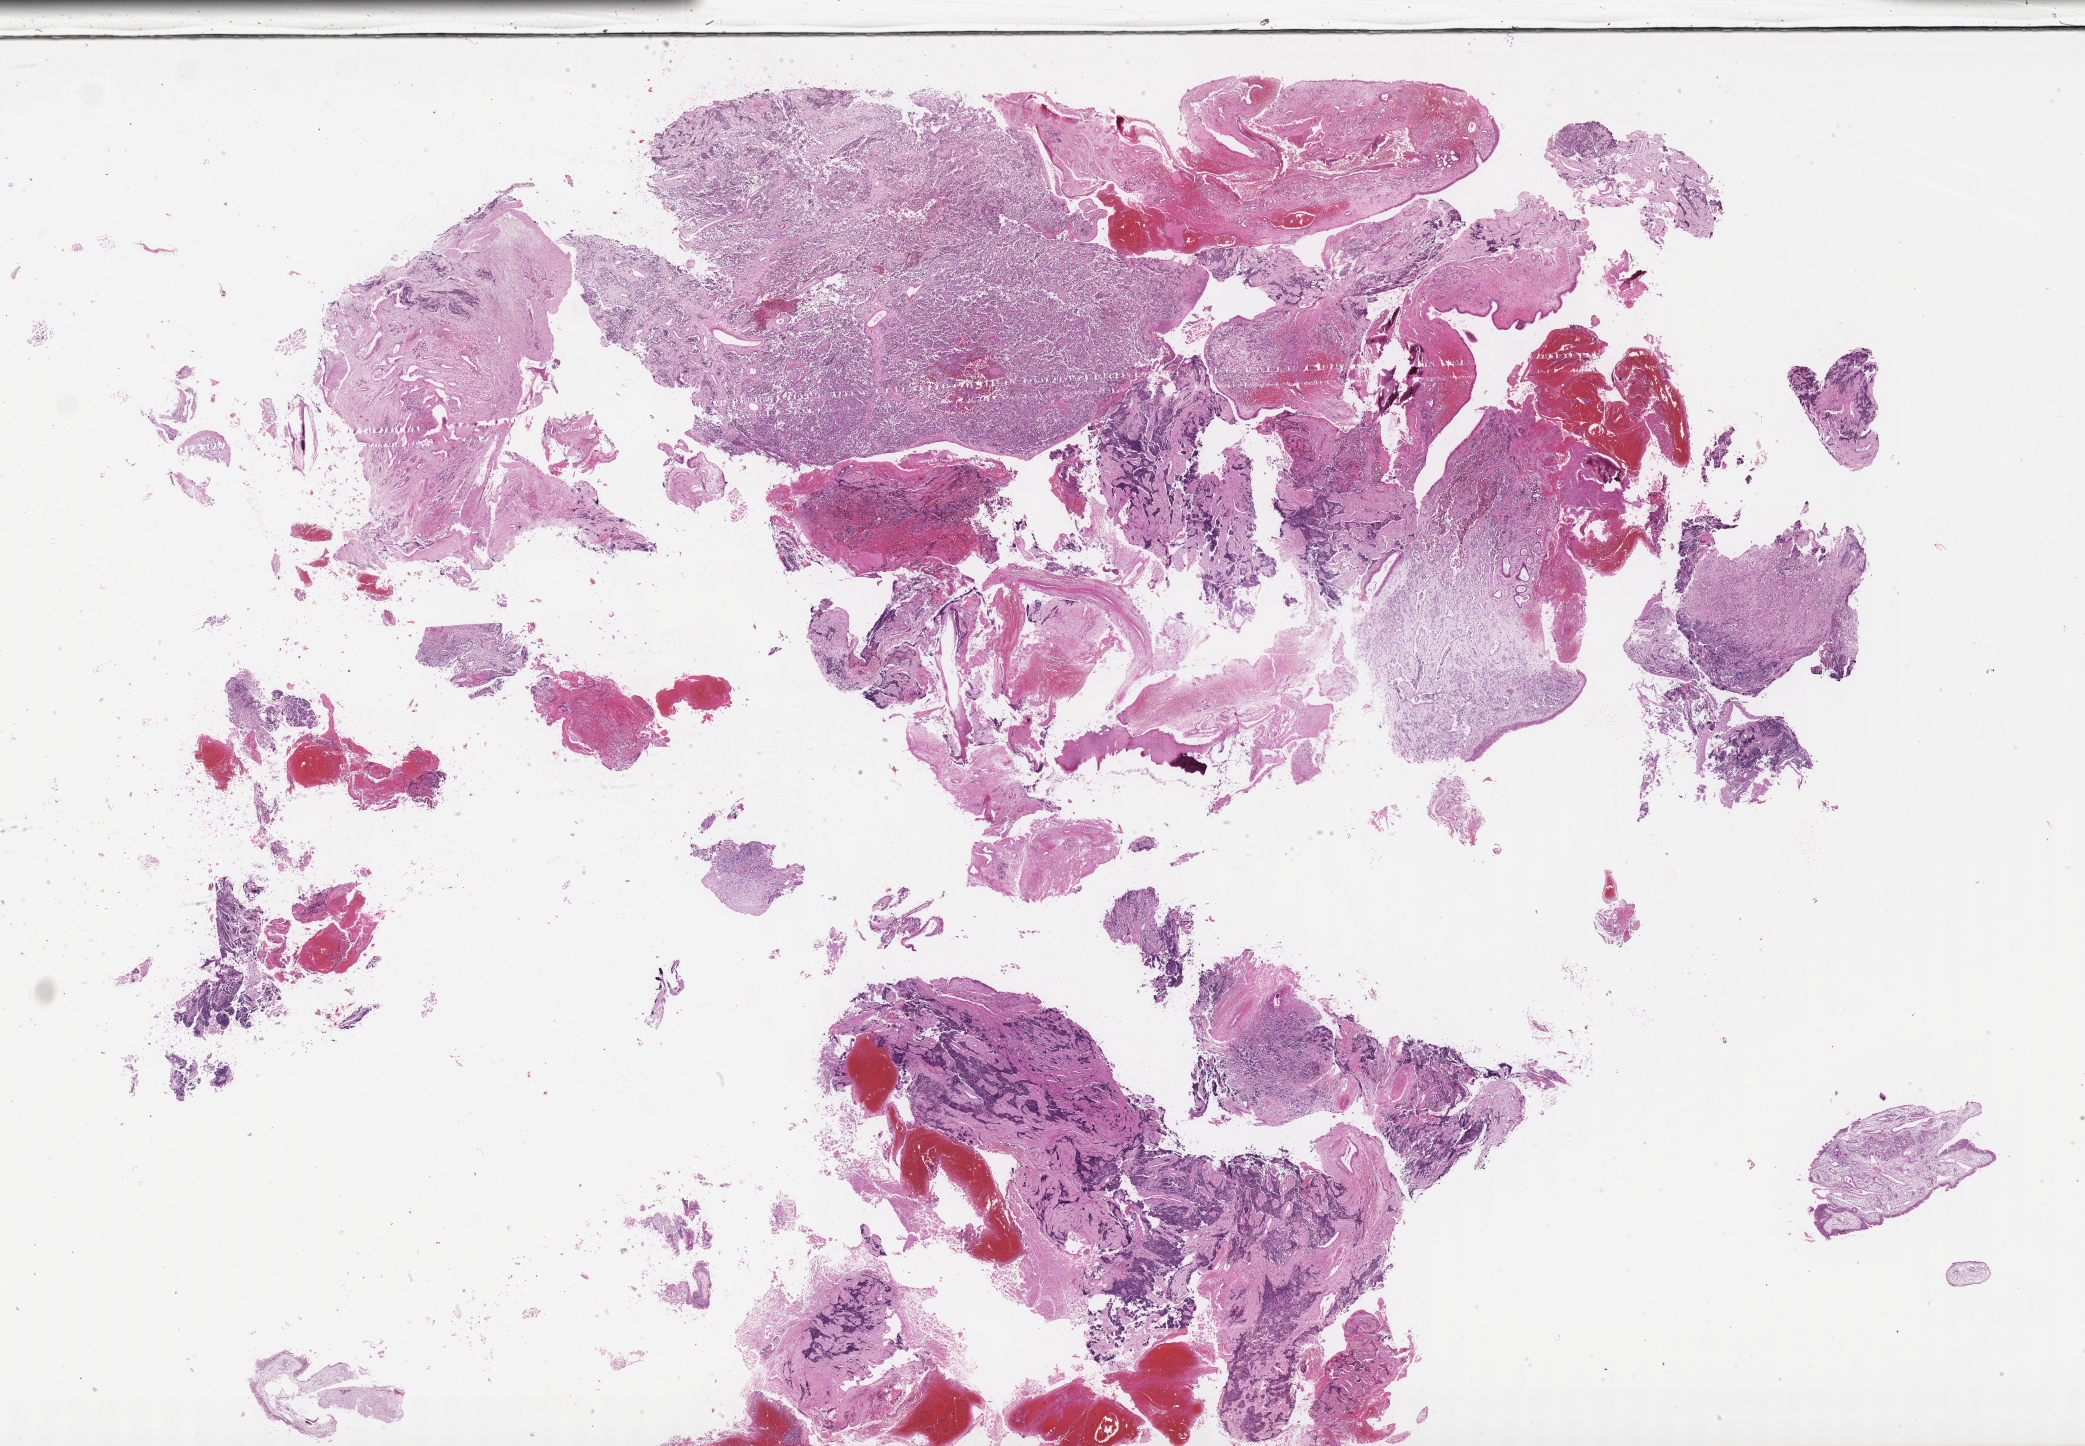
Hematoxylin and eosin (H&E) whole-slide image of tumor tissue — whole scanned area (about 33.7 x 23.4 mm) shown as a low-resolution overview; formalin-fixed paraffin-embedded section; site: nasal mass, left. Patient: male, age 17.9 years at diagnosis.
Primary site (case record): nasal Cavity & Sinus. Diagnosis: rhabdomyosarcoma; histological classification: alveolar rhabdomyosarcoma. Metastatic status at presentation (as recorded): non-metastatic. Stage (as recorded): 2.